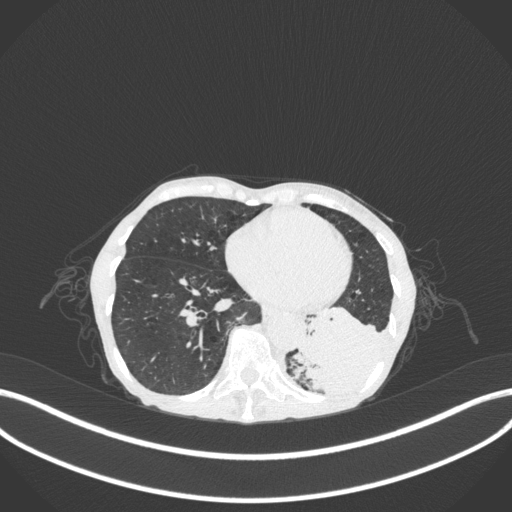
Chest CT, one axial slice. Slice 86 of 347 in the series (ordered by position). Reconstruction kernel B31f. Lung window (W 1500 / L -600 HU). 1 mm slice thickness. 512 × 512 image matrix, field of view 400 × 400 mm. Female patient, age 70 years. From the clinical record (not read from this slice): clinical TNM (as recorded): T3 N0 M0; histopathological grade: G3.
Annotated regions visible in this slice (bounding box drawn by a radiologist):
- lung tumour (recorded histology: small cell carcinoma): bounding box <288,297,395,405> (left, top, right, bottom; pixels)